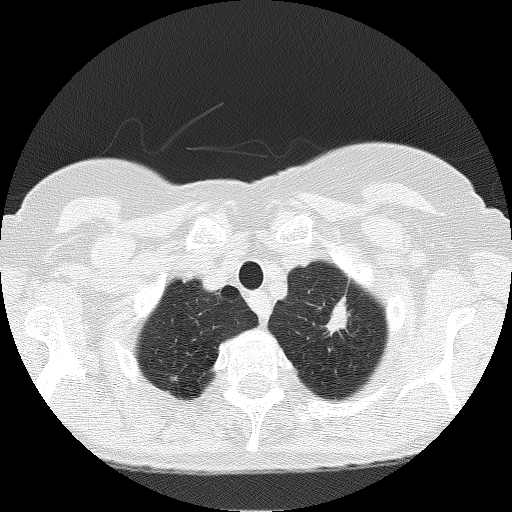
Axial slice from a low-dose chest CT screening exam, baseline screening round, lung window (W 1500 / L -600 HU), 2 mm slice thickness, 512 × 512 image matrix, field of view 303 × 303 mm. Female participant, aged 66 years at enrolment. Current smoker at enrolment.
Expert reader's lesion annotation, bounding box [x1, y1, x2, y2] px = [312, 287, 368, 346]. The screening reader recorded 3 non-calcified nodules or masses ≥4 mm on this exam (left upper lobe, left upper lobe, left upper lobe); which of them this box marks is not recorded. Official screen result: positive, change unspecified: nodule(s) >= 4 mm or enlarging nodule(s), mass(es), or other non-specific abnormalities suspicious for lung cancer. Lung cancer was diagnosed 156 days after this screen: adenocarcinoma, NOS, left upper lobe, moderately differentiated (G2), stage IB (AJCC 6th edition), 17 mm at pathology.